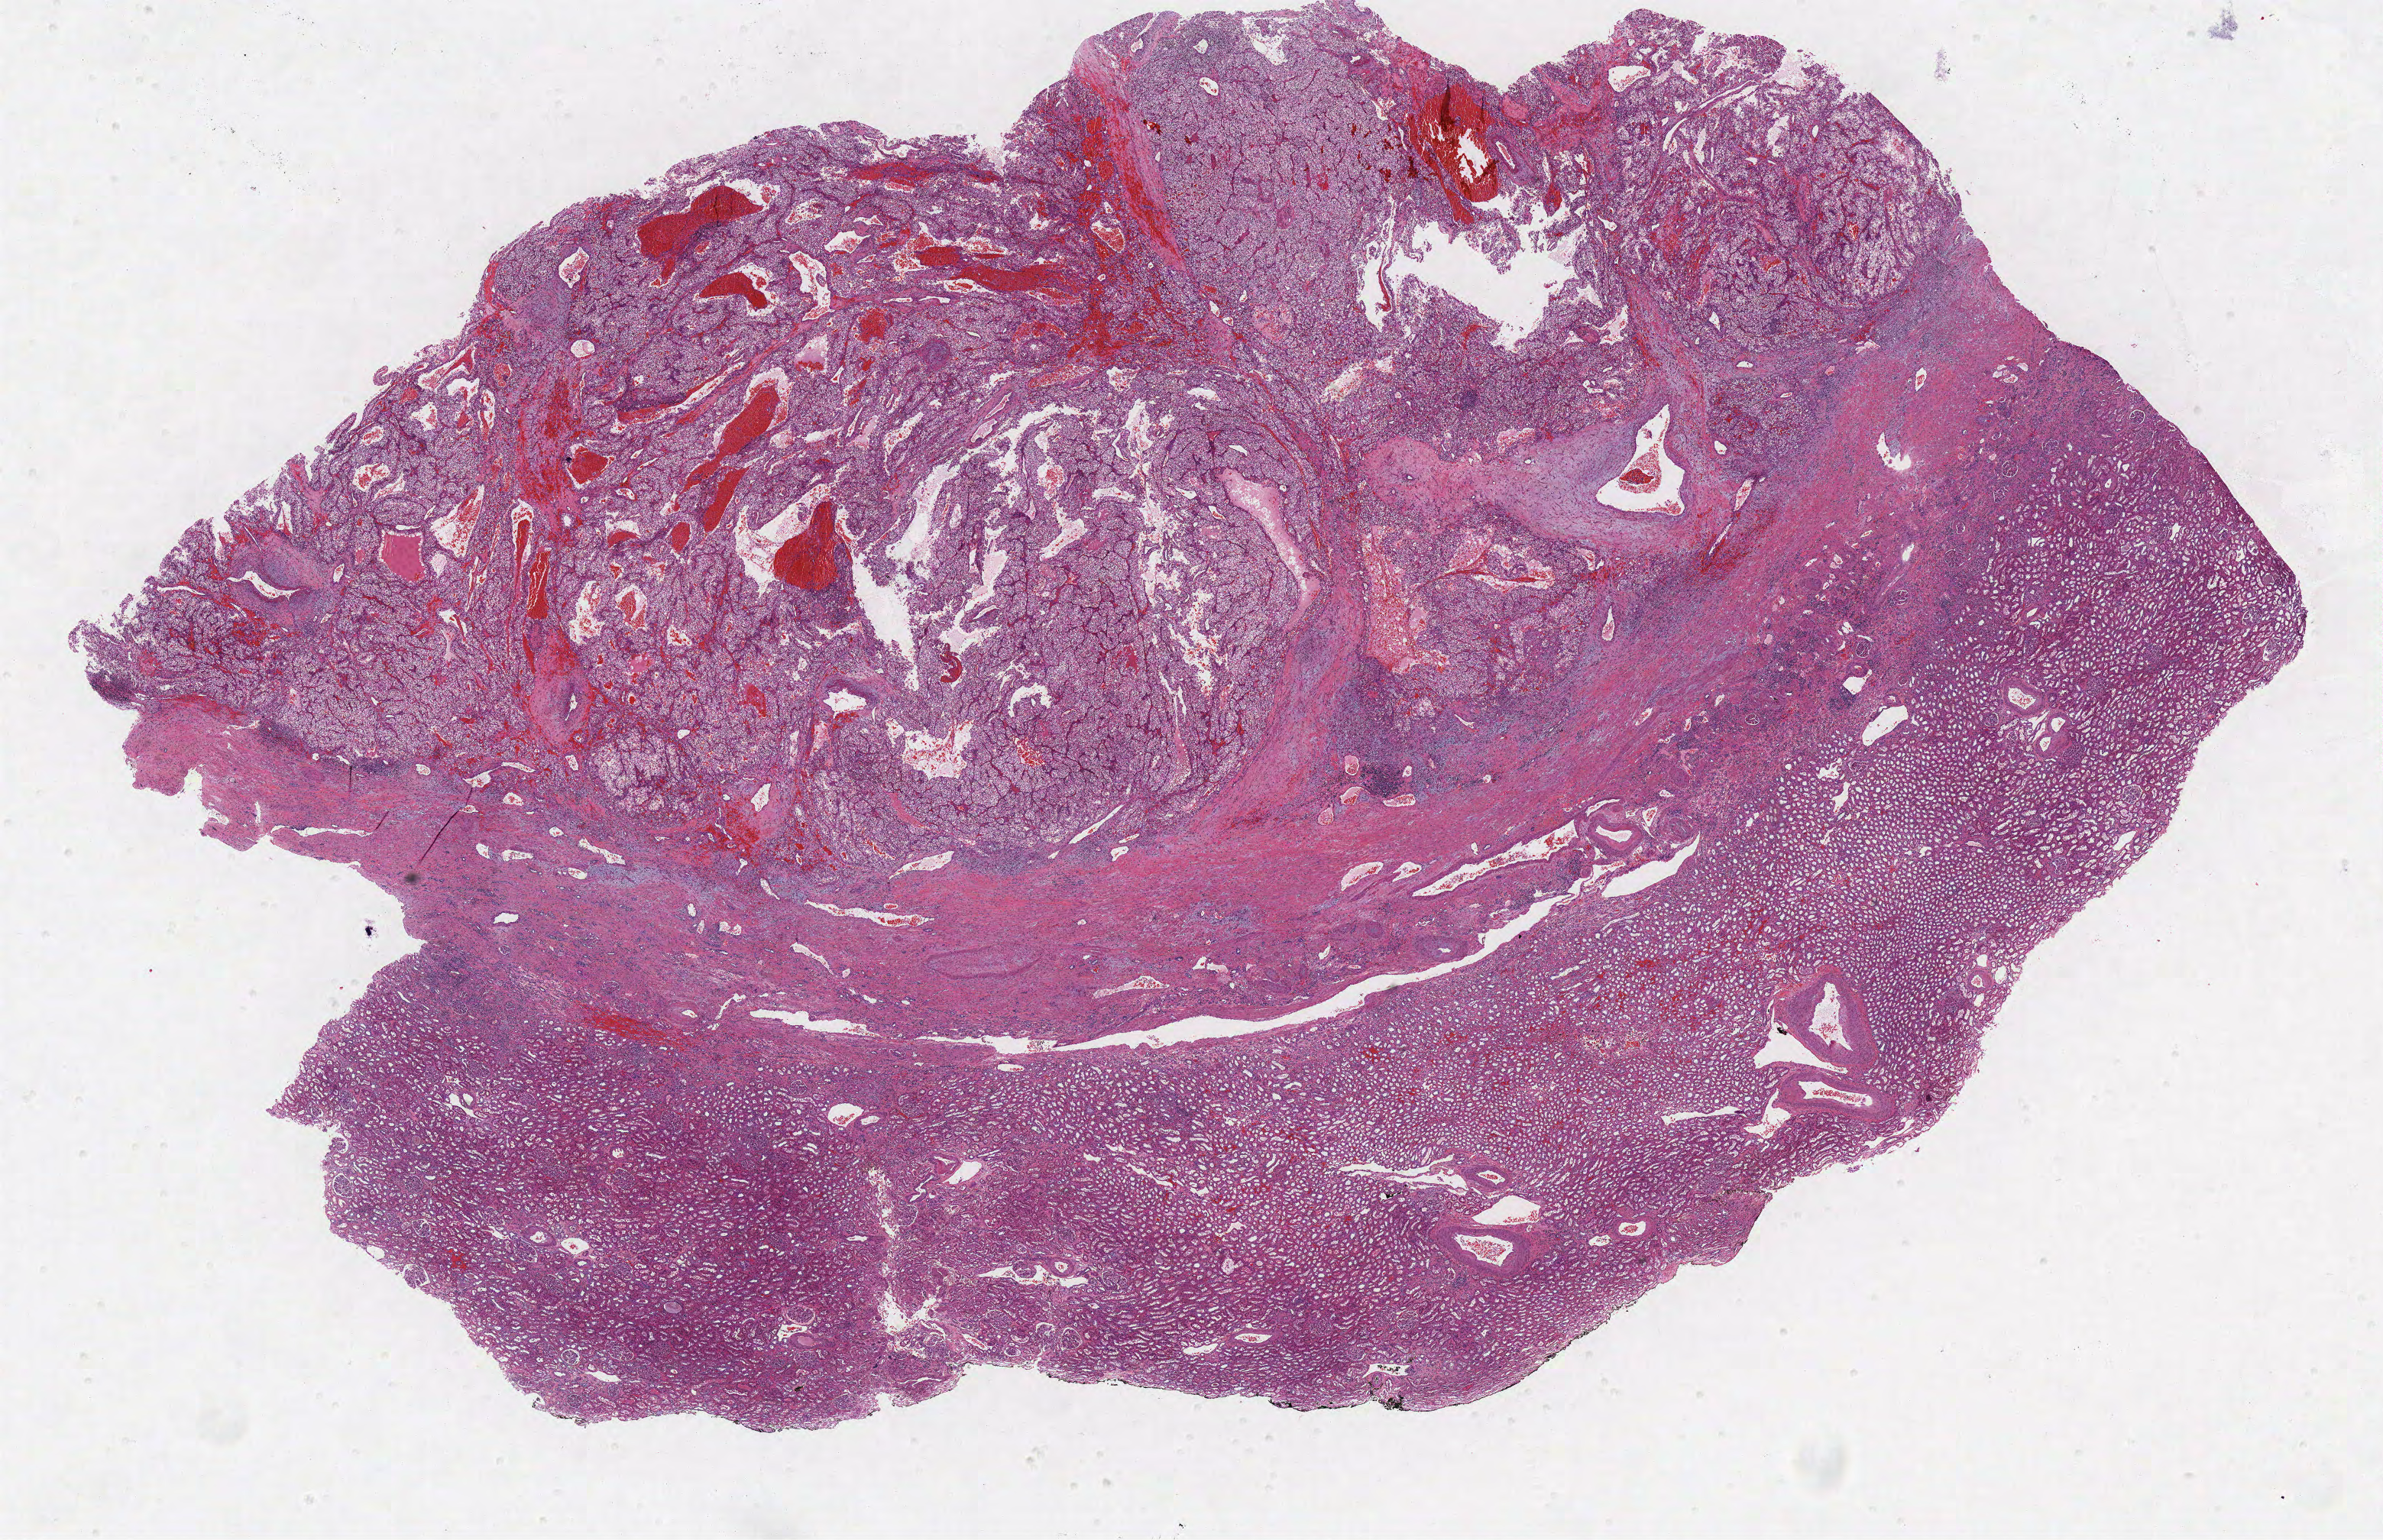
H&E whole-slide image — low-resolution overview of the scanned area, about 24.9 x 16.1 mm (acquisition: 40x scan), FFPE section, kidney, primary tumour sample. Patient: male, age at initial diagnosis 53 years. Histologic grade: G2 (moderately differentiated).
Laterality: right. TNM: T1a NX M0. Pathologic diagnosis: Clear cell adenocarcinoma, NOS. AJCC pathologic stage: I.